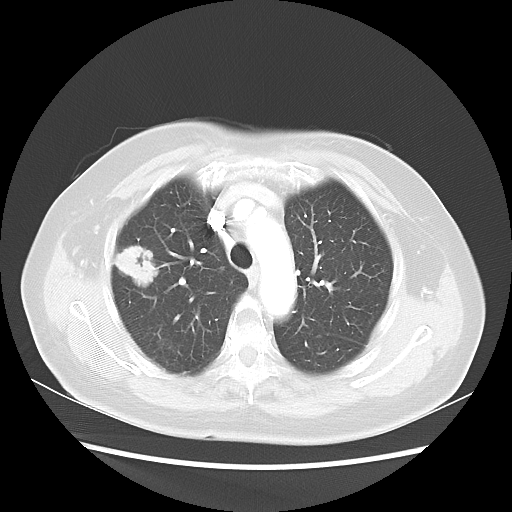
Chest CT, one axial slice; slice 35 of 48 in the series (ordered by position); reconstruction kernel LUNG; 100 kVp; lung window (W 1500 / L -600 HU); 5 mm slice thickness; 512 × 512 image matrix. Female patient, age 75 years. From the clinical record (not read from this slice): clinical TNM (as recorded): T1c N0 M0.
Outlined on this slice (rectangle marked by the reading radiologist):
- lung tumour (recorded histology: adenocarcinoma): bounding box [x1, y1, x2, y2] px = [112, 239, 163, 294]